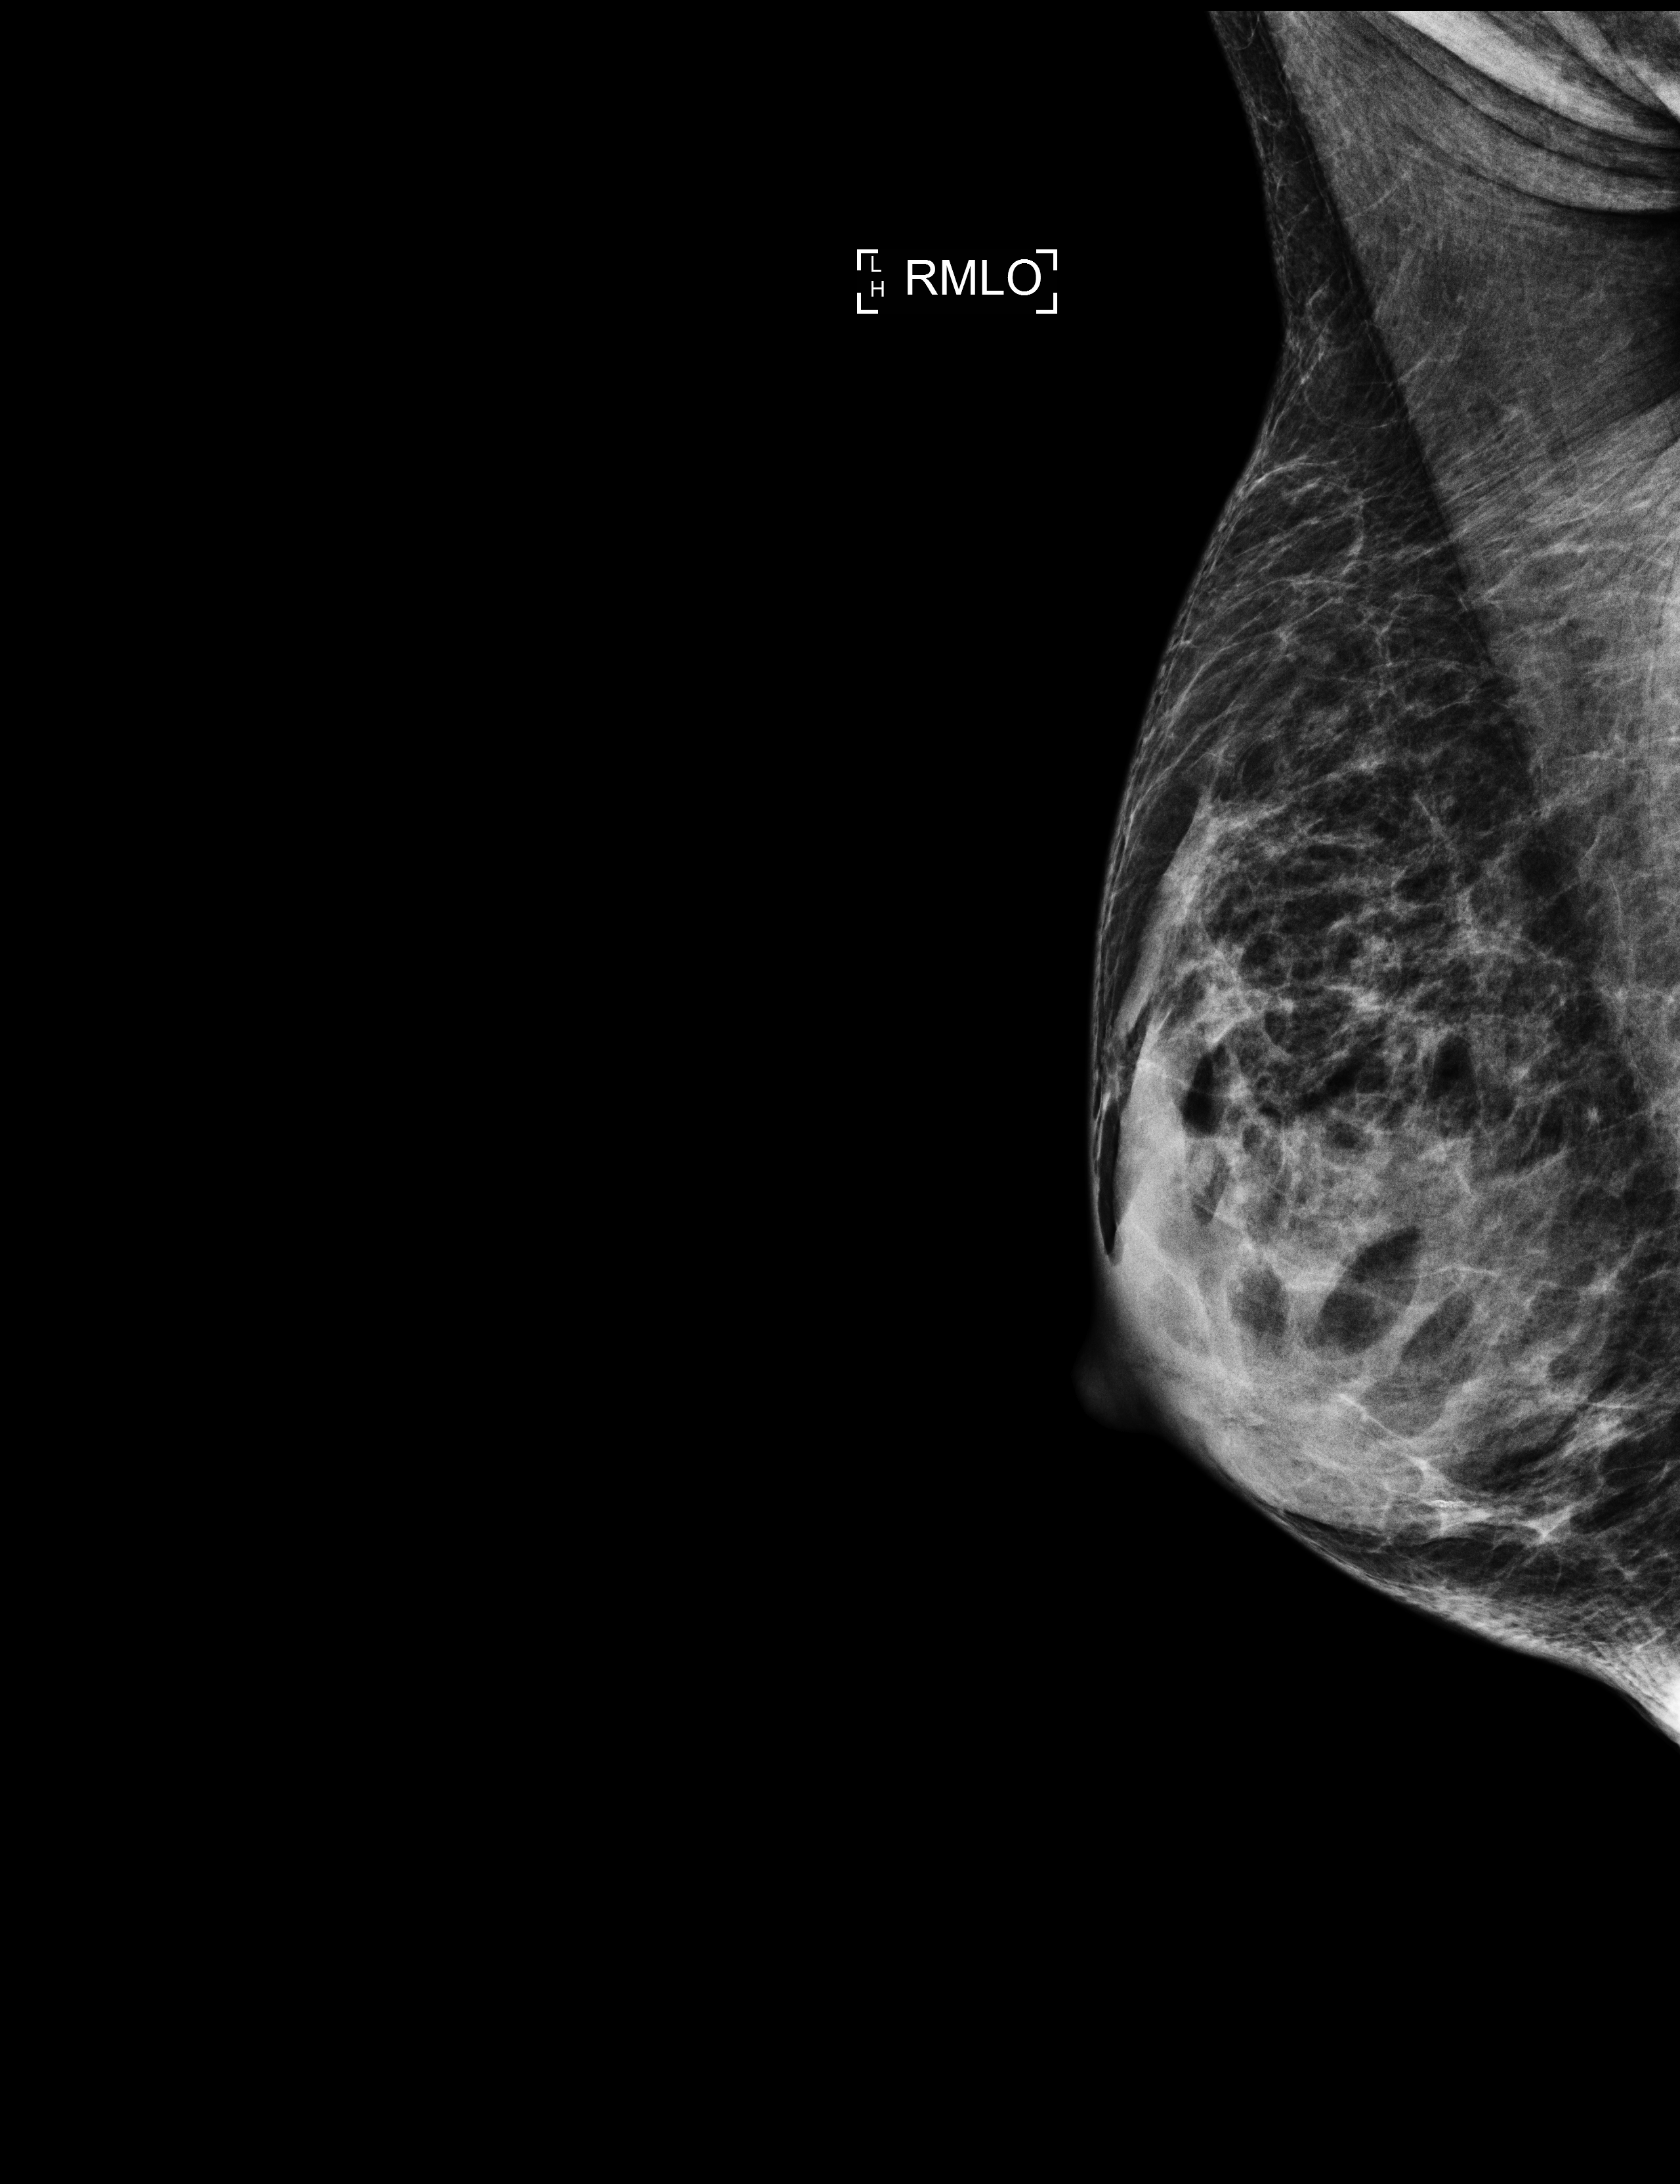
Screening examination; compressed breast thickness 30 mm. Patient: female, 67 years.
Image type: full-field digital mammogram. Breast: right. Projection: medio-lateral oblique projection.